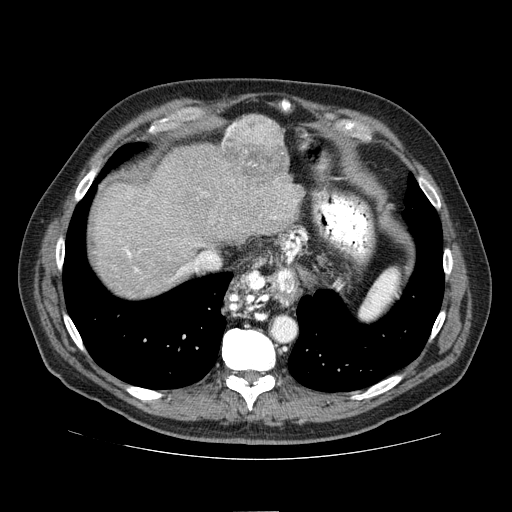
Contrast-enhanced abdominal CT (liver protocol), one axial slice; slice 62 of 81 in the series (ordered by position); reconstruction kernel STANDARD; one of 2 acquisitions stored at this slice position; soft-tissue window (W 400 / L 40 HU); 512 × 512 image matrix. From the clinical record (not read from this slice): diagnosis: hepatocellular carcinoma (patient treated with transarterial chemoembolisation; whether this scan precedes or follows treatment is not stated here); TNM stage (as recorded): Stage-IIIA; Child-Pugh class: A.
Annotated regions visible in this slice (semi-automatic segmentation, software-assisted and operator-edited):
- abdominal aorta: bounding box [x1, y1, x2, y2] px = [273, 317, 295, 341]
- liver parenchyma outside the tumour (the mass and vessels are separate outlines, so this box may not span the whole liver): [93, 116, 302, 298]
- mass: [220, 114, 288, 184]
- liver vessels: [124, 200, 296, 276]